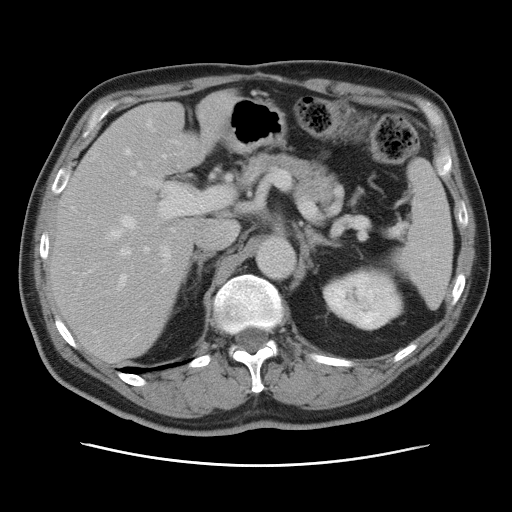
Contrast-enhanced abdominal CT, one axial slice. 120 kVp. Intravenous contrast given. Soft-tissue window (W 400 / L 40 HU). 5 mm slice thickness. 512 × 512 image matrix, field of view 370 × 370 mm. Male patient, age 69 years. Case-level facts recorded for this patient, not image findings: diagnosis: colorectal cancer liver metastases, imaged before liver resection; multiple liver metastases: no; largest metastasis: 5 cm; chemotherapy before resection: no.
Annotated regions visible in this slice (expert manual segmentation):
- hepatic veins: bounding box (x1, y1, x2, y2) in pixels: (95, 122, 167, 335)
- liver: (50, 93, 236, 361)
- planned liver remnant (the part of the liver to remain after resection): (50, 93, 236, 360)
- portal vein (with intrahepatic branches): (118, 141, 205, 272)